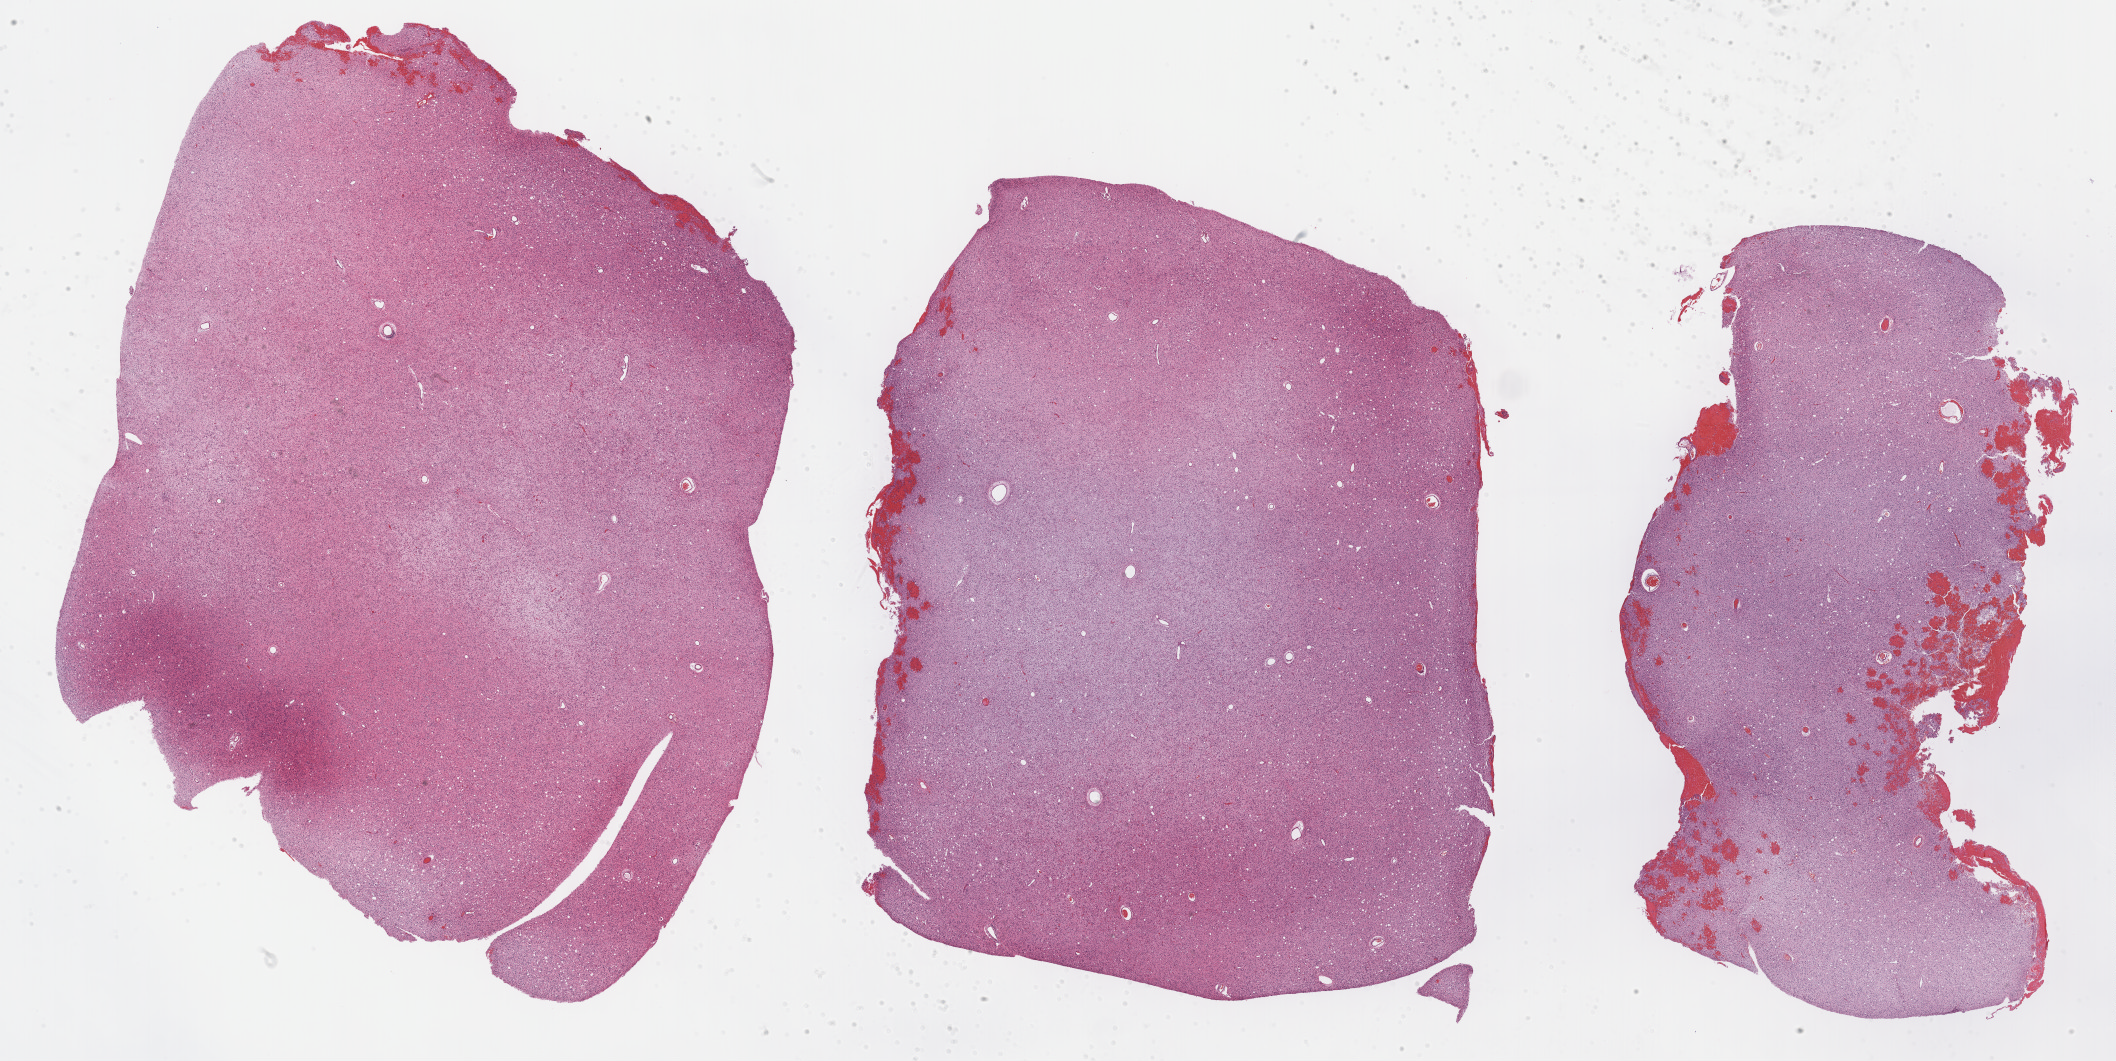
Whole-slide histology image, H&E-stained, whole scanned area (about 34.2 x 17.2 mm, slide scanned at 40x) shown as a low-resolution overview, formalin-fixed paraffin-embedded (FFPE) diagnostic section, sample: primary tumour, brain. Patient: female, age at initial diagnosis 24 years. Histologic grade: G2 (moderately differentiated).
Pathologic diagnosis: Astrocytoma, NOS.